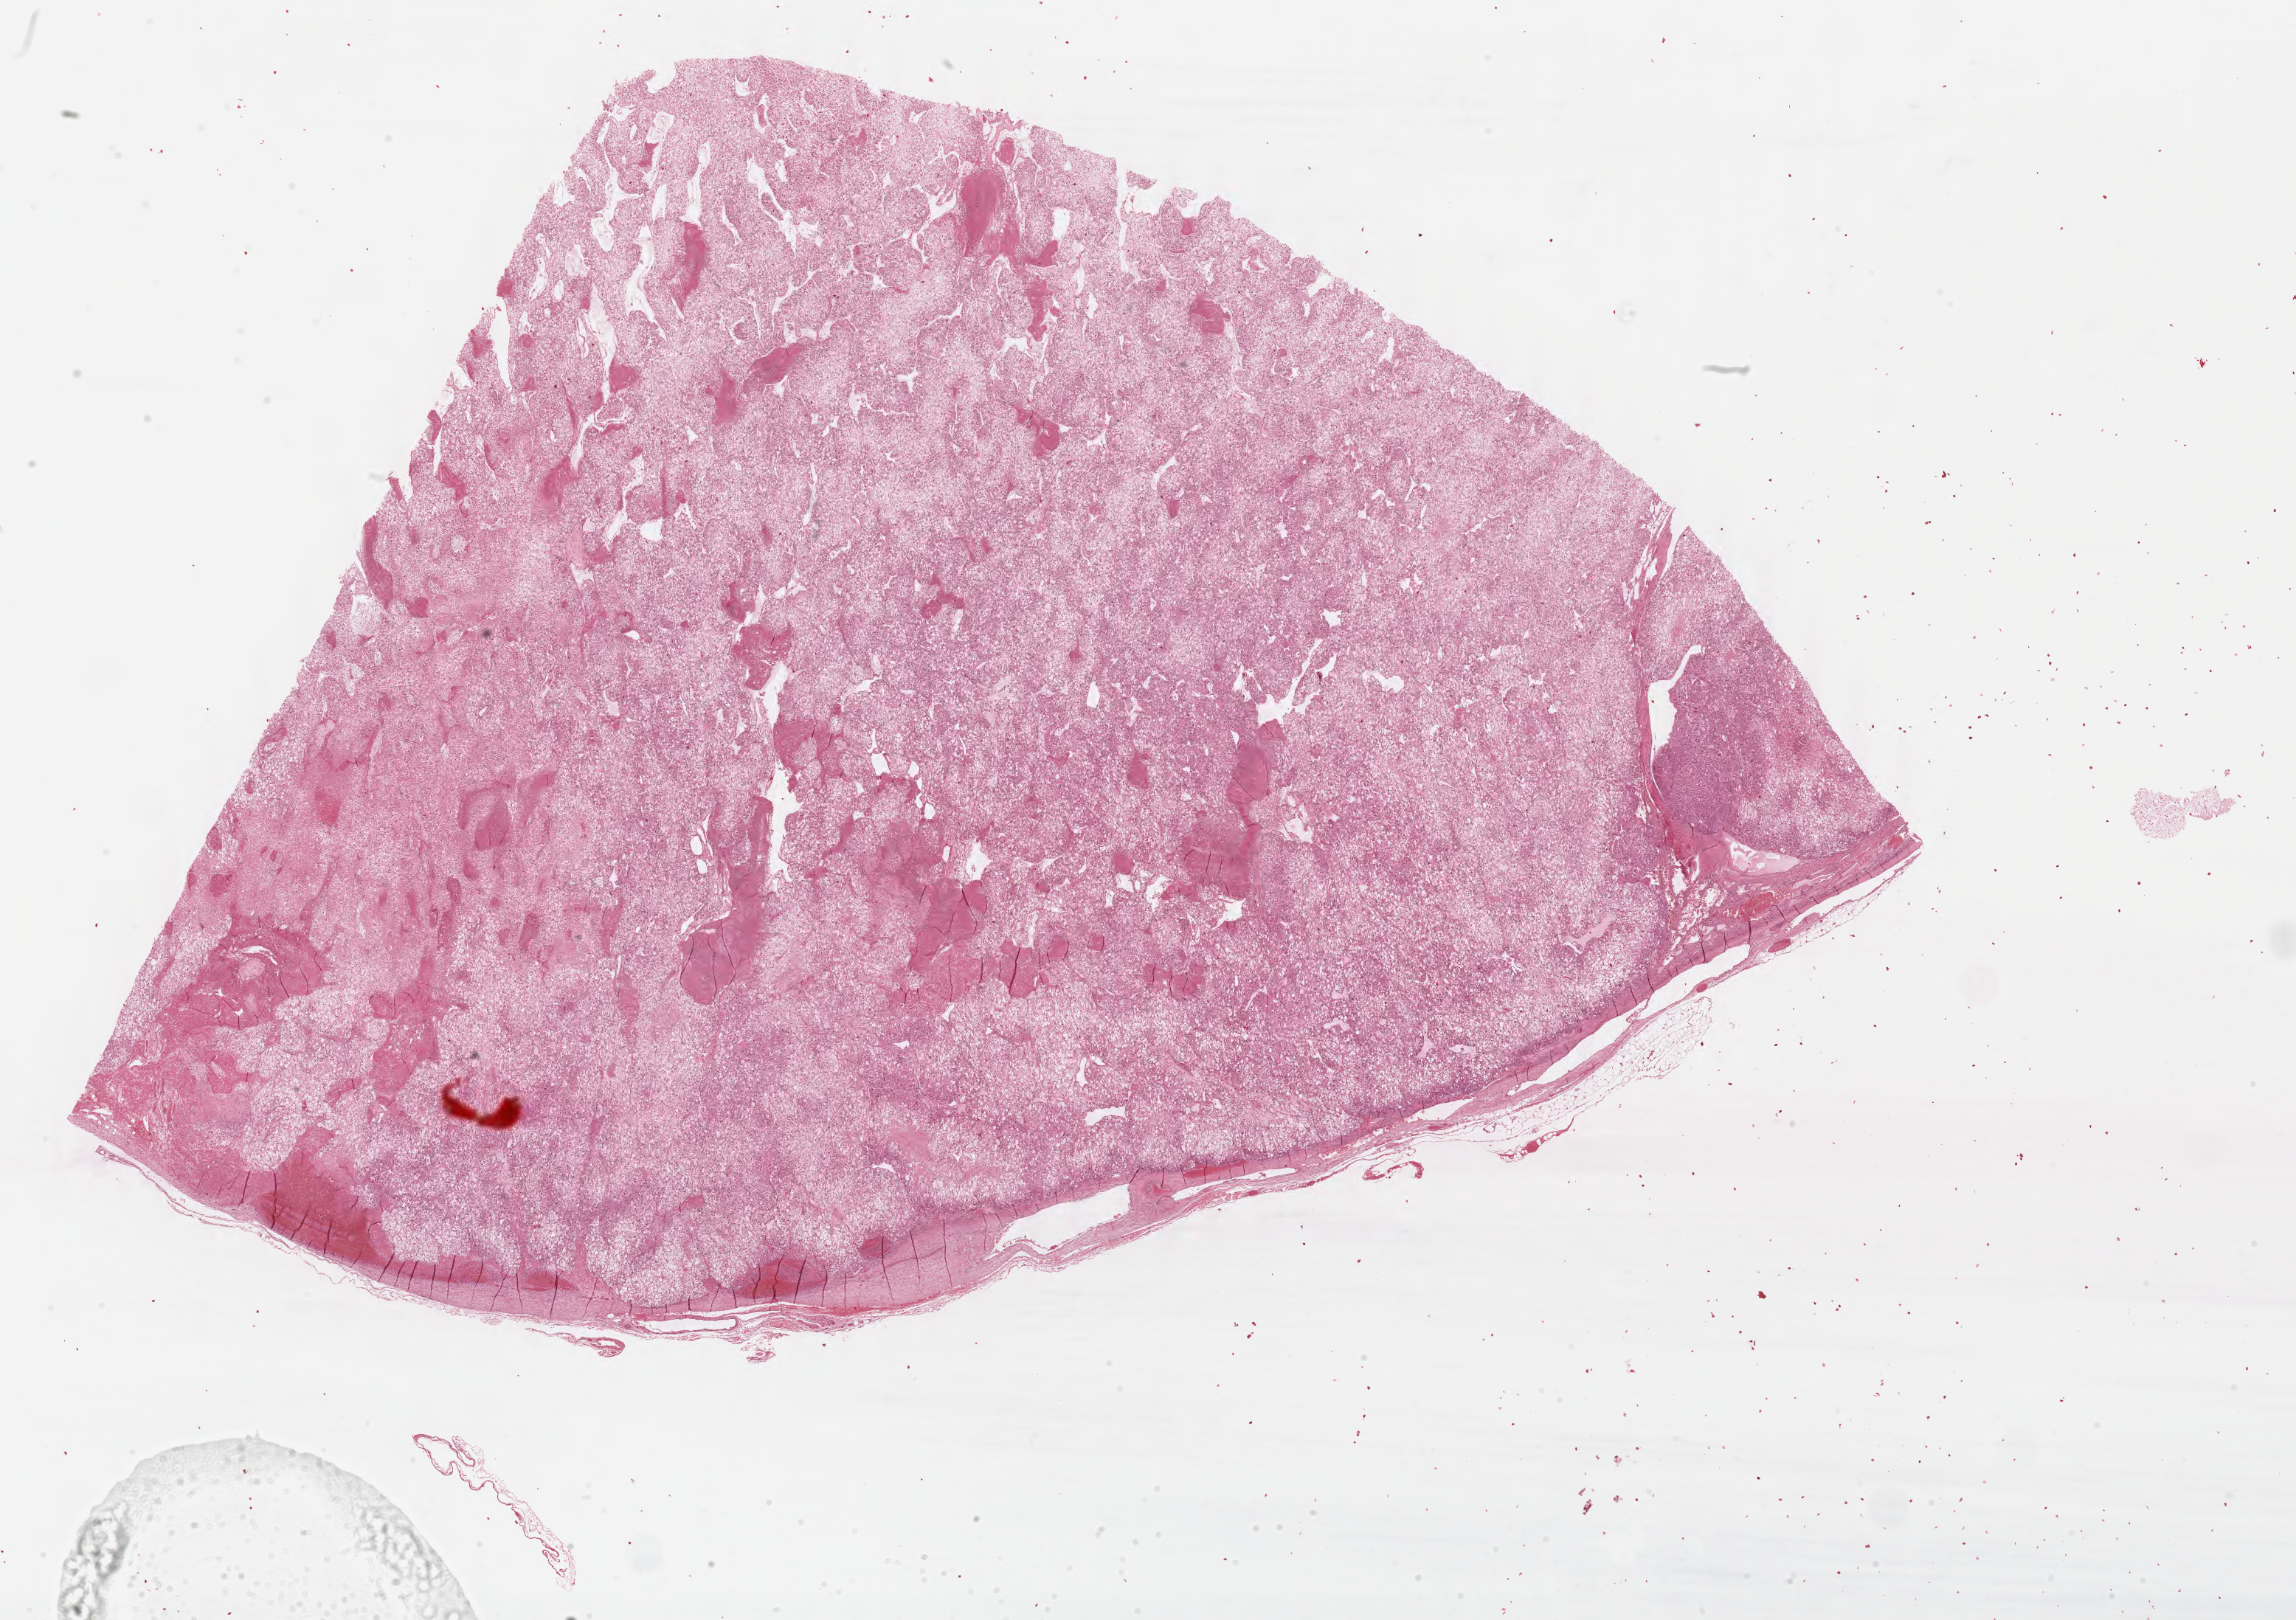
Whole-slide histology image, H&E-stained — a low-resolution overview of the entire scanned area, about 24.6 x 17.3 mm. Formalin-fixed paraffin-embedded (FFPE) diagnostic section. Adrenal cortex, primary tumour sample. Female patient; age at initial diagnosis 44 years.
Lymph nodes positive (case pathology): 0 of 3 examined. Histologic diagnosis: Adrenal cortical carcinoma (cortex of adrenal gland).